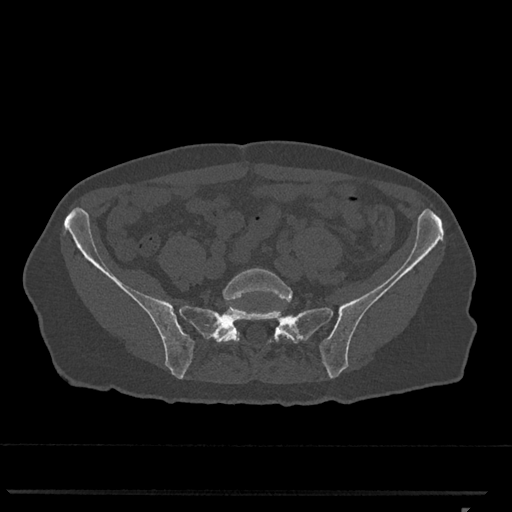
CT including the spine, one axial slice. Slice 120 of 793 in the series (ordered by position). Reconstruction kernel Br40s/3. 120 kVp. Bone window (W 1800 / L 400 HU). 0.5 mm slice thickness. 512 × 512 image matrix, field of view 380 × 380 mm. Female patient, age 62 years. Case-level facts recorded for this patient, not image findings: primary cancer: renal.
Annotated regions visible in this slice (semi-automatic segmentation, software-assisted and operator-edited):
- L5 vertebra: bounding box <222,268,297,343> (left, top, right, bottom; pixels)